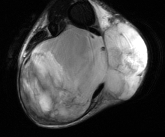
MRI of an extremity soft-tissue mass, one axial slice; position 31 of 81 along the scan axis; T2-weighted fat-saturated; MR volume resampled by the dataset authors to the PET/CT grid (not the native acquisition matrix); 3.27 mm slice thickness; 165 × 137 image matrix, field of view 161 × 134 mm. Male patient. Case-level facts recorded for this patient, not image findings: histological type: liposarcoma - round cell; grade: high; site of the primary tumour: right calf.
Structures marked on this image (expert contour drawn on MRI and transferred to this co-registered scan by the dataset authors):
- gross tumour volume (mass): bounding box [x1, y1, x2, y2] px = [21, 21, 147, 120]